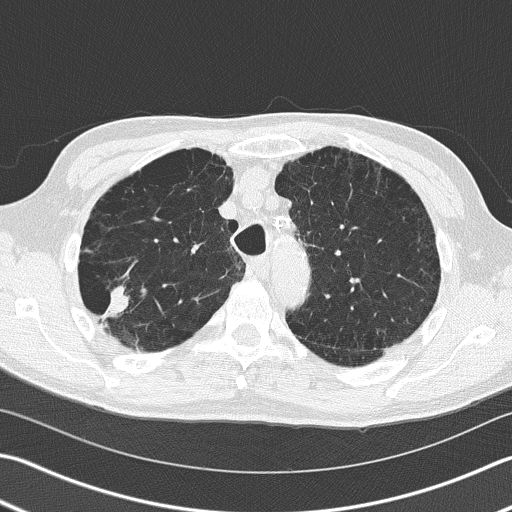
Low-dose screening chest CT, one axial slice; position 121 of 163 along the scan axis; 120 kVp; lung window (W 1500 / L -600 HU); 2 mm slice thickness; 512 × 512 image matrix, field of view 346 × 346 mm.
Outlined on this slice (expert manual segmentation):
- lesion 1 (tumor, upper lobe of right lung): bounding box [x1, y1, x2, y2] px = [104, 286, 129, 319]